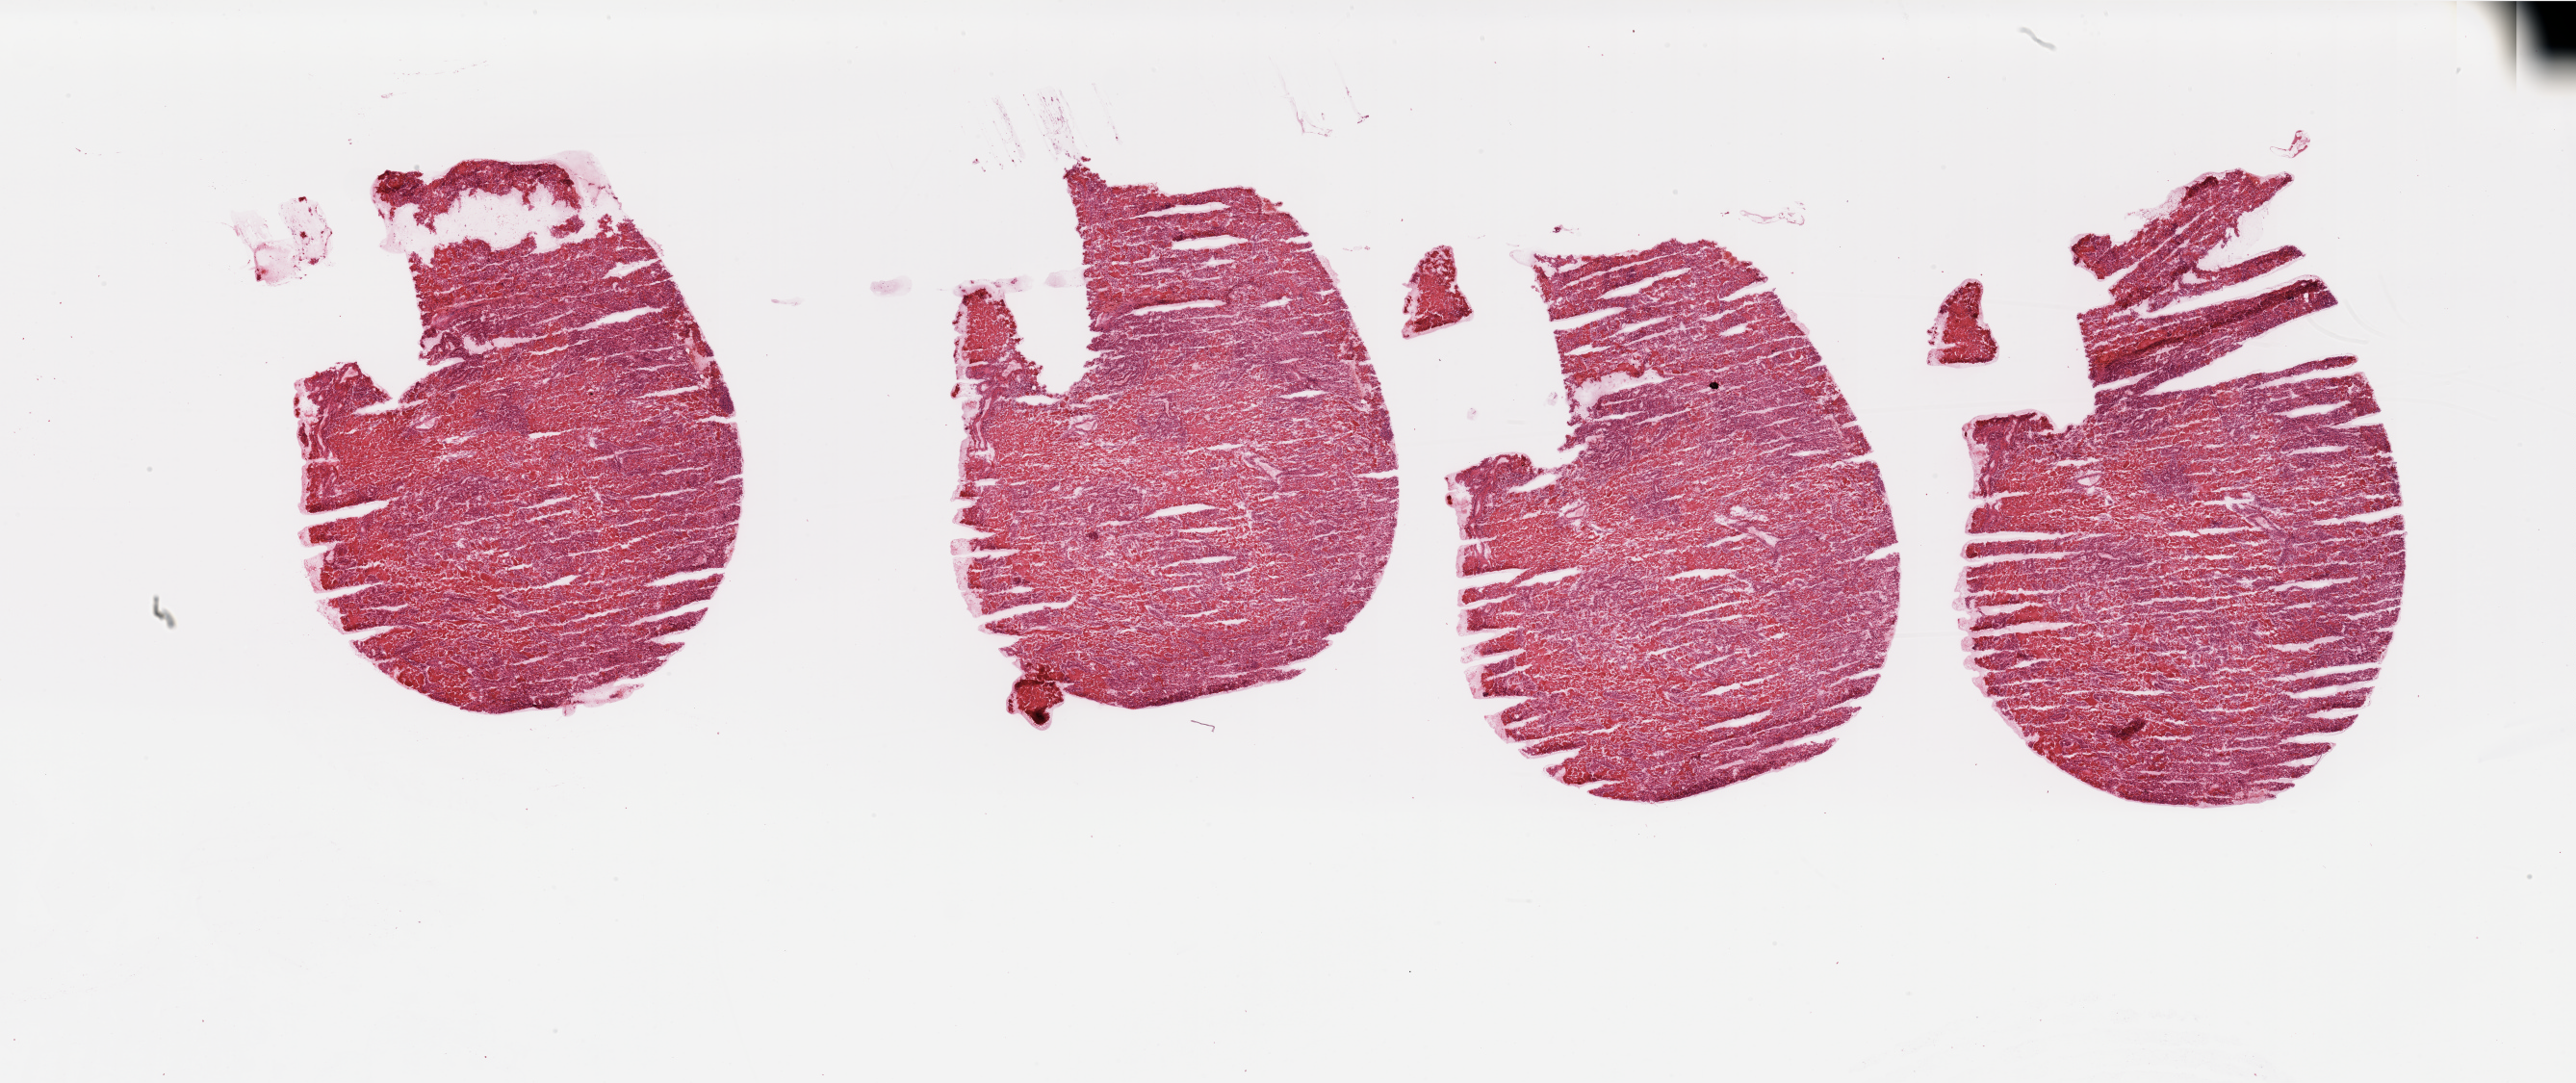
Digitized H&E-stained tissue section (whole slide), low-resolution overview of the scanned area, about 42.3 x 17.8 mm, tumour tissue sample, sampled site: kidney. Patient: female, age 69 years.
Diagnosis: Renal cell carcinoma, NOS.